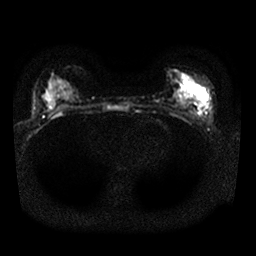
Breast MRI, one axial slice. Slice 10 of 25 in the series (ordered by position). Diffusion-weighted series; image 2 of 4 stored at this slice position (different b-values; order by instance number). 1.5 T. 256 × 256 image matrix. Female patient.
Structures marked on this image (manually delineated by an expert):
- tumour on diffusion-weighted imaging: bounding box <201,91,206,98> (left, top, right, bottom; pixels)